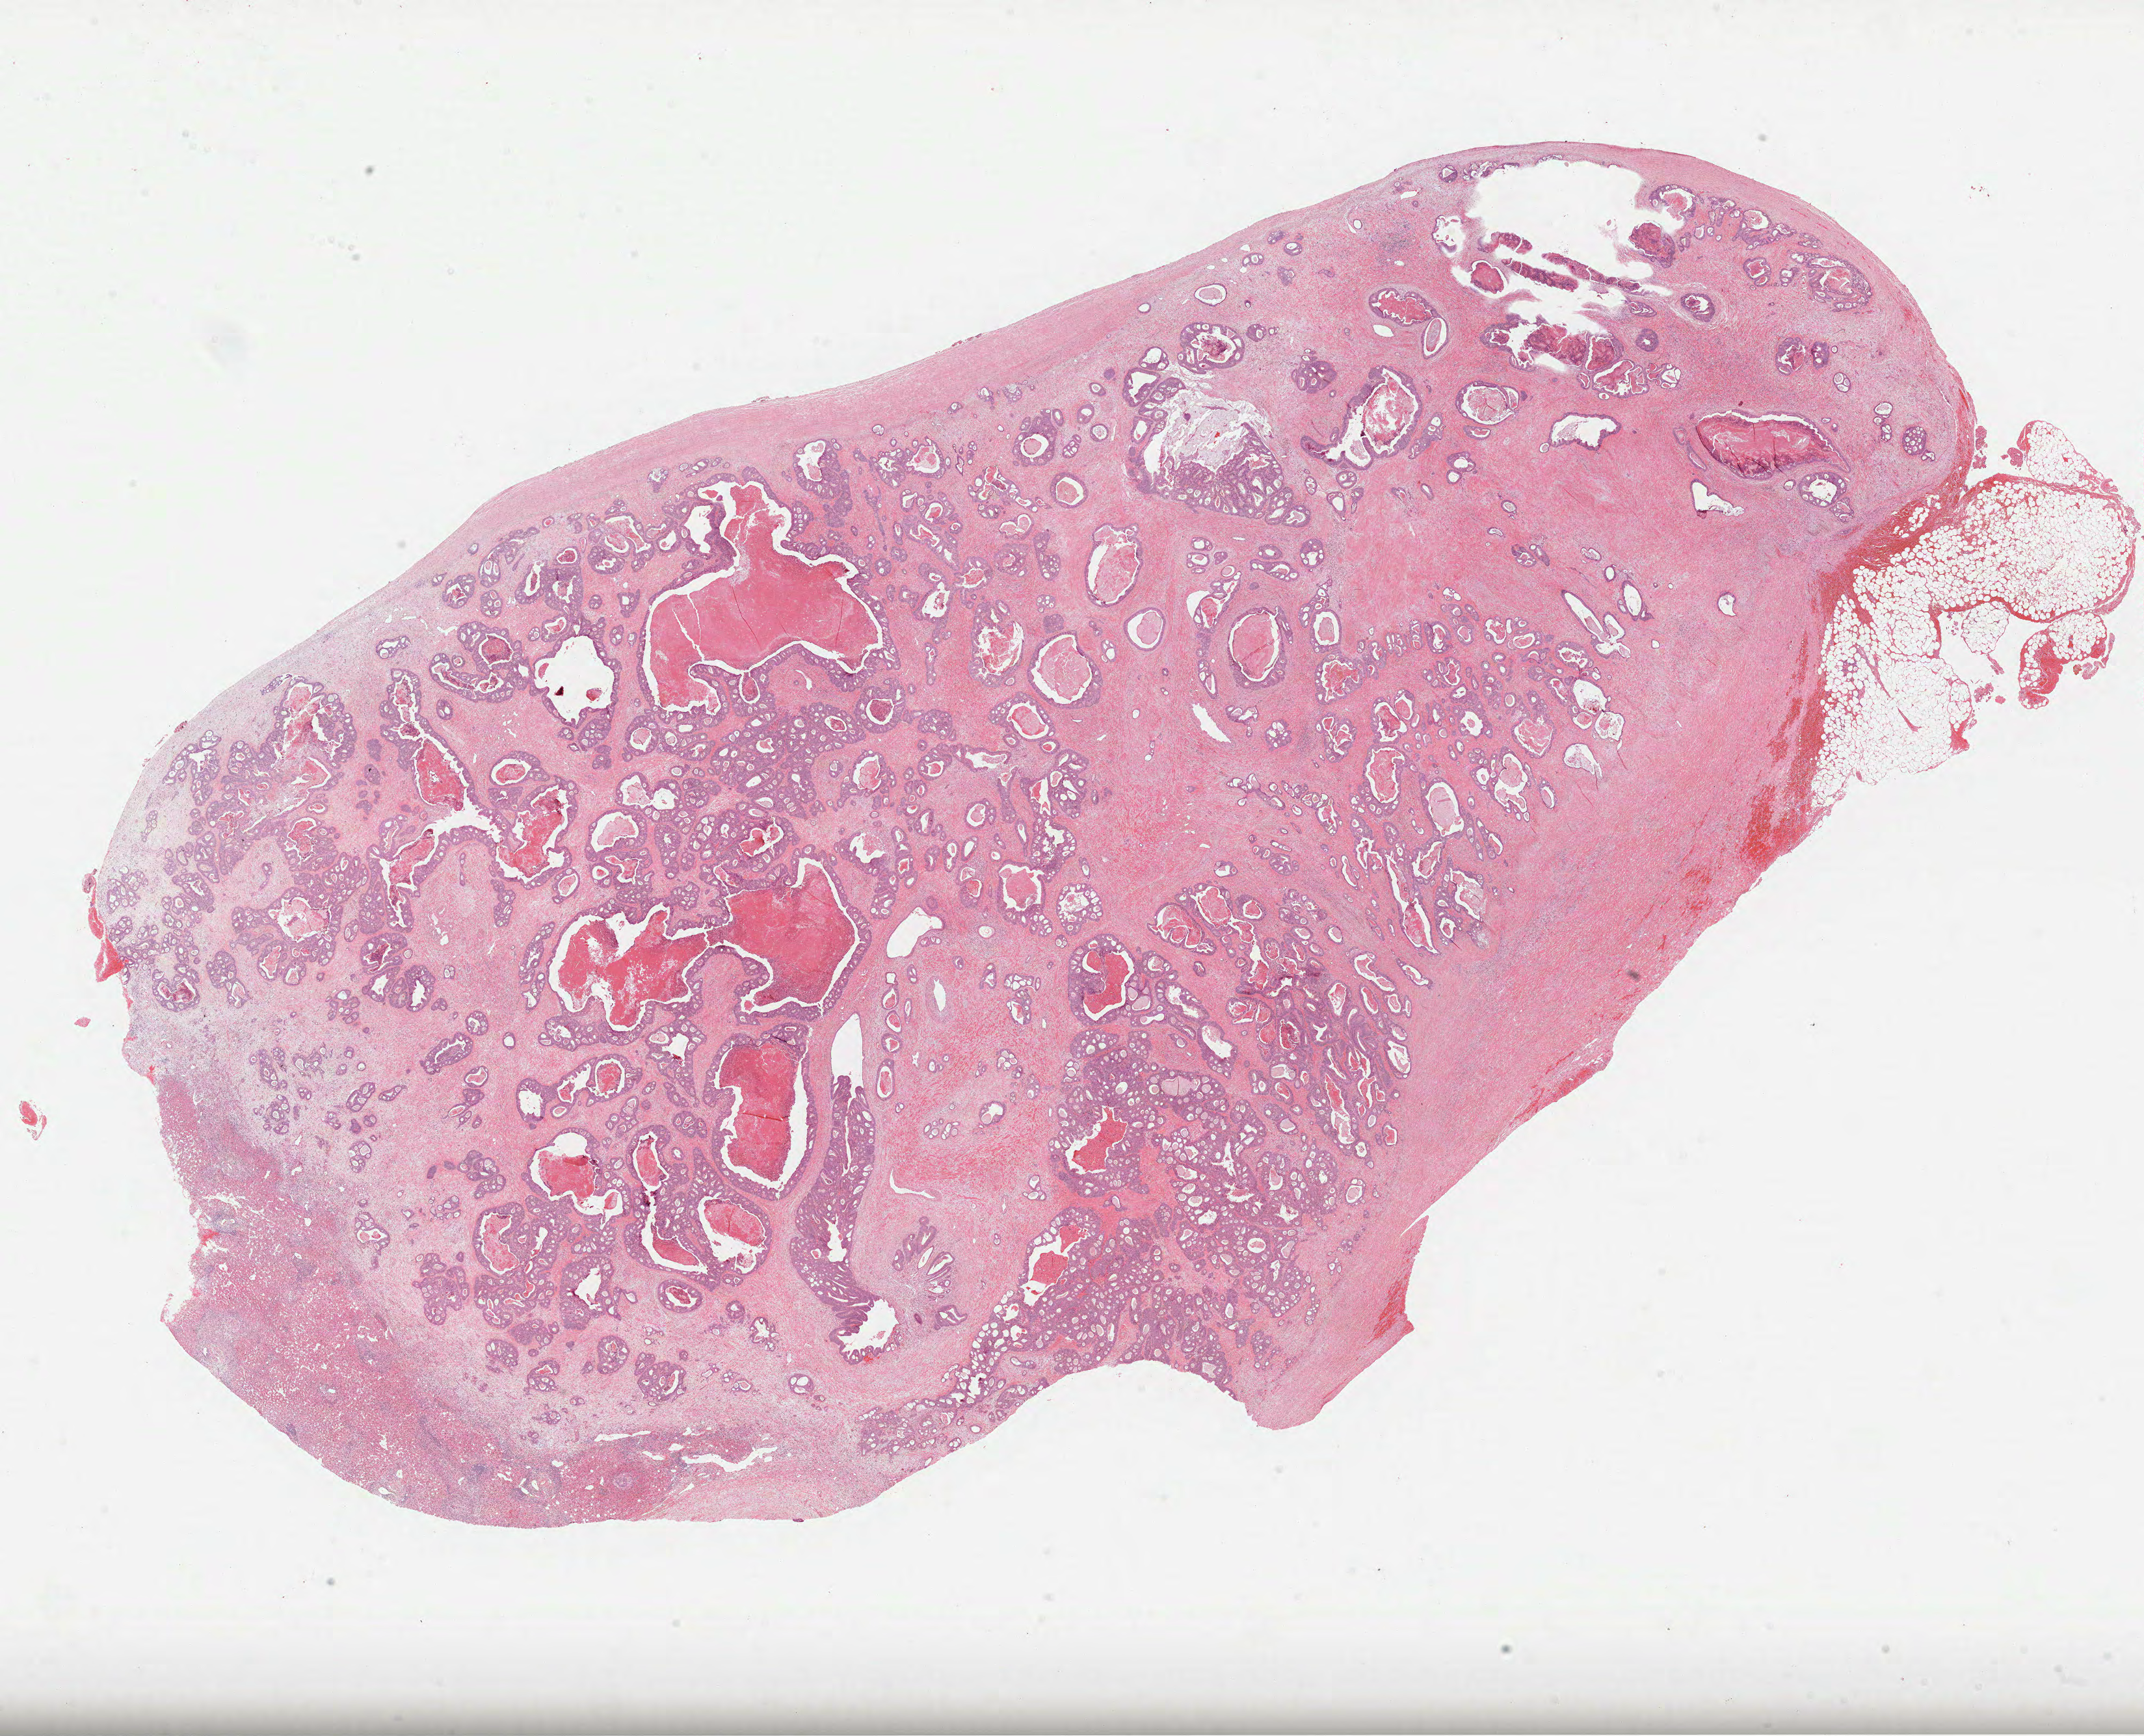
Whole-slide histology image, H&E-stained, whole scanned area (about 26.6 x 21.5 mm, acquisition: 40x scan) shown as a low-resolution overview. Formalin-fixed paraffin-embedded (FFPE) diagnostic section. Primary tumour sample from the rectum. Patient: male, age at initial diagnosis 56 years.
Histologic diagnosis: Adenocarcinoma, NOS (rectosigmoid junction).